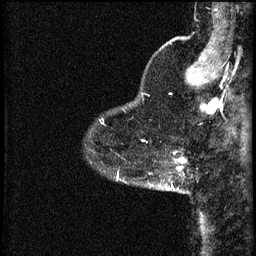
Breast MRI (dynamic contrast-enhanced), one sagittal slice; position 9 of 60 along the scan axis; 3 images stored at this slice position (order not interpretable as contrast timing); 1.5 T; TE 4.2 ms, TR 8.2 ms; 2 mm slice thickness; 256 × 256 image matrix, field of view 200 × 200 mm. Patient: female, 37 years.
Structures marked on this image (semi-automatically segmented with operator editing):
- analysis volume of interest (the breast-tissue region the enhancement analysis was run in; not a lesion): bounding box <150,154,185,193> (left, top, right, bottom; pixels)
- tumour enhancement mask (voxels above the 70 % enhancement threshold inside the analysis volume of interest): <174,154,185,171>